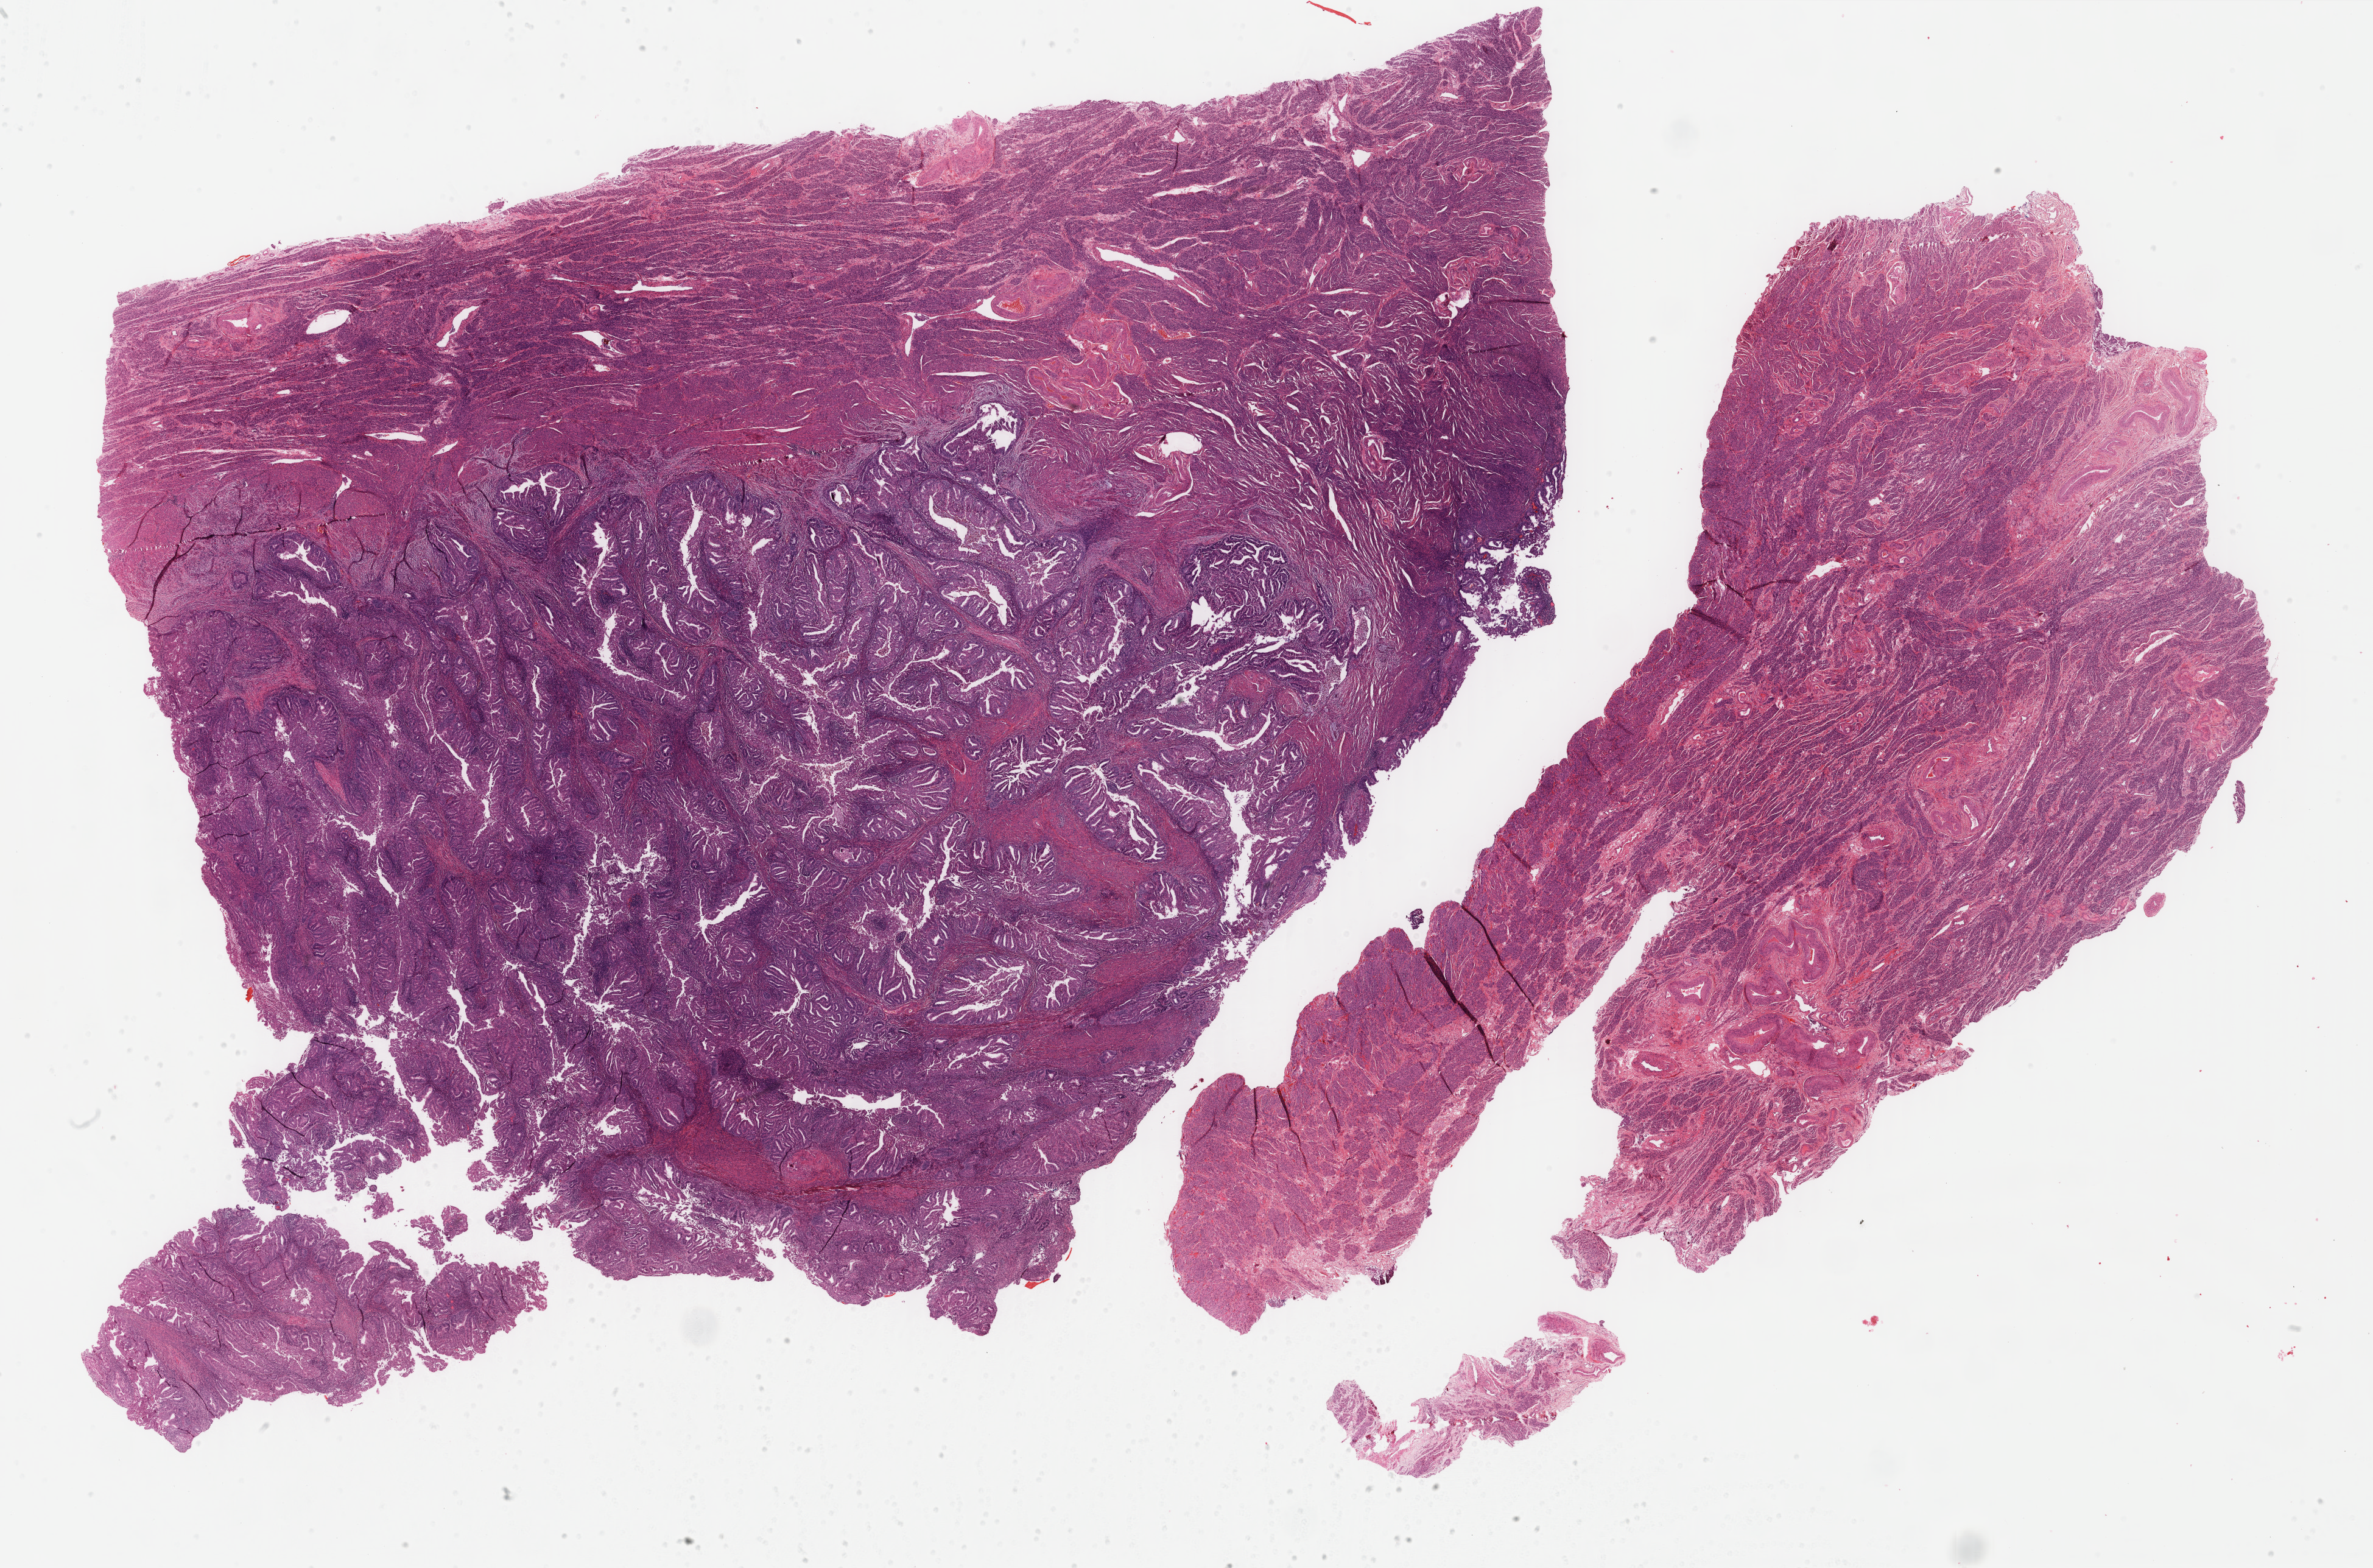
Whole-slide histology image, H&E-stained, a low-resolution overview of the entire scanned area, about 30.9 x 20.4 mm. Formalin-fixed paraffin-embedded (FFPE) diagnostic section. Uterus, primary tumour sample. Patient: female, age at initial diagnosis 81 years. Histologic grade: G2 (moderately differentiated).
Histologic diagnosis: Endometrioid adenocarcinoma, NOS. FIGO stage: IB.